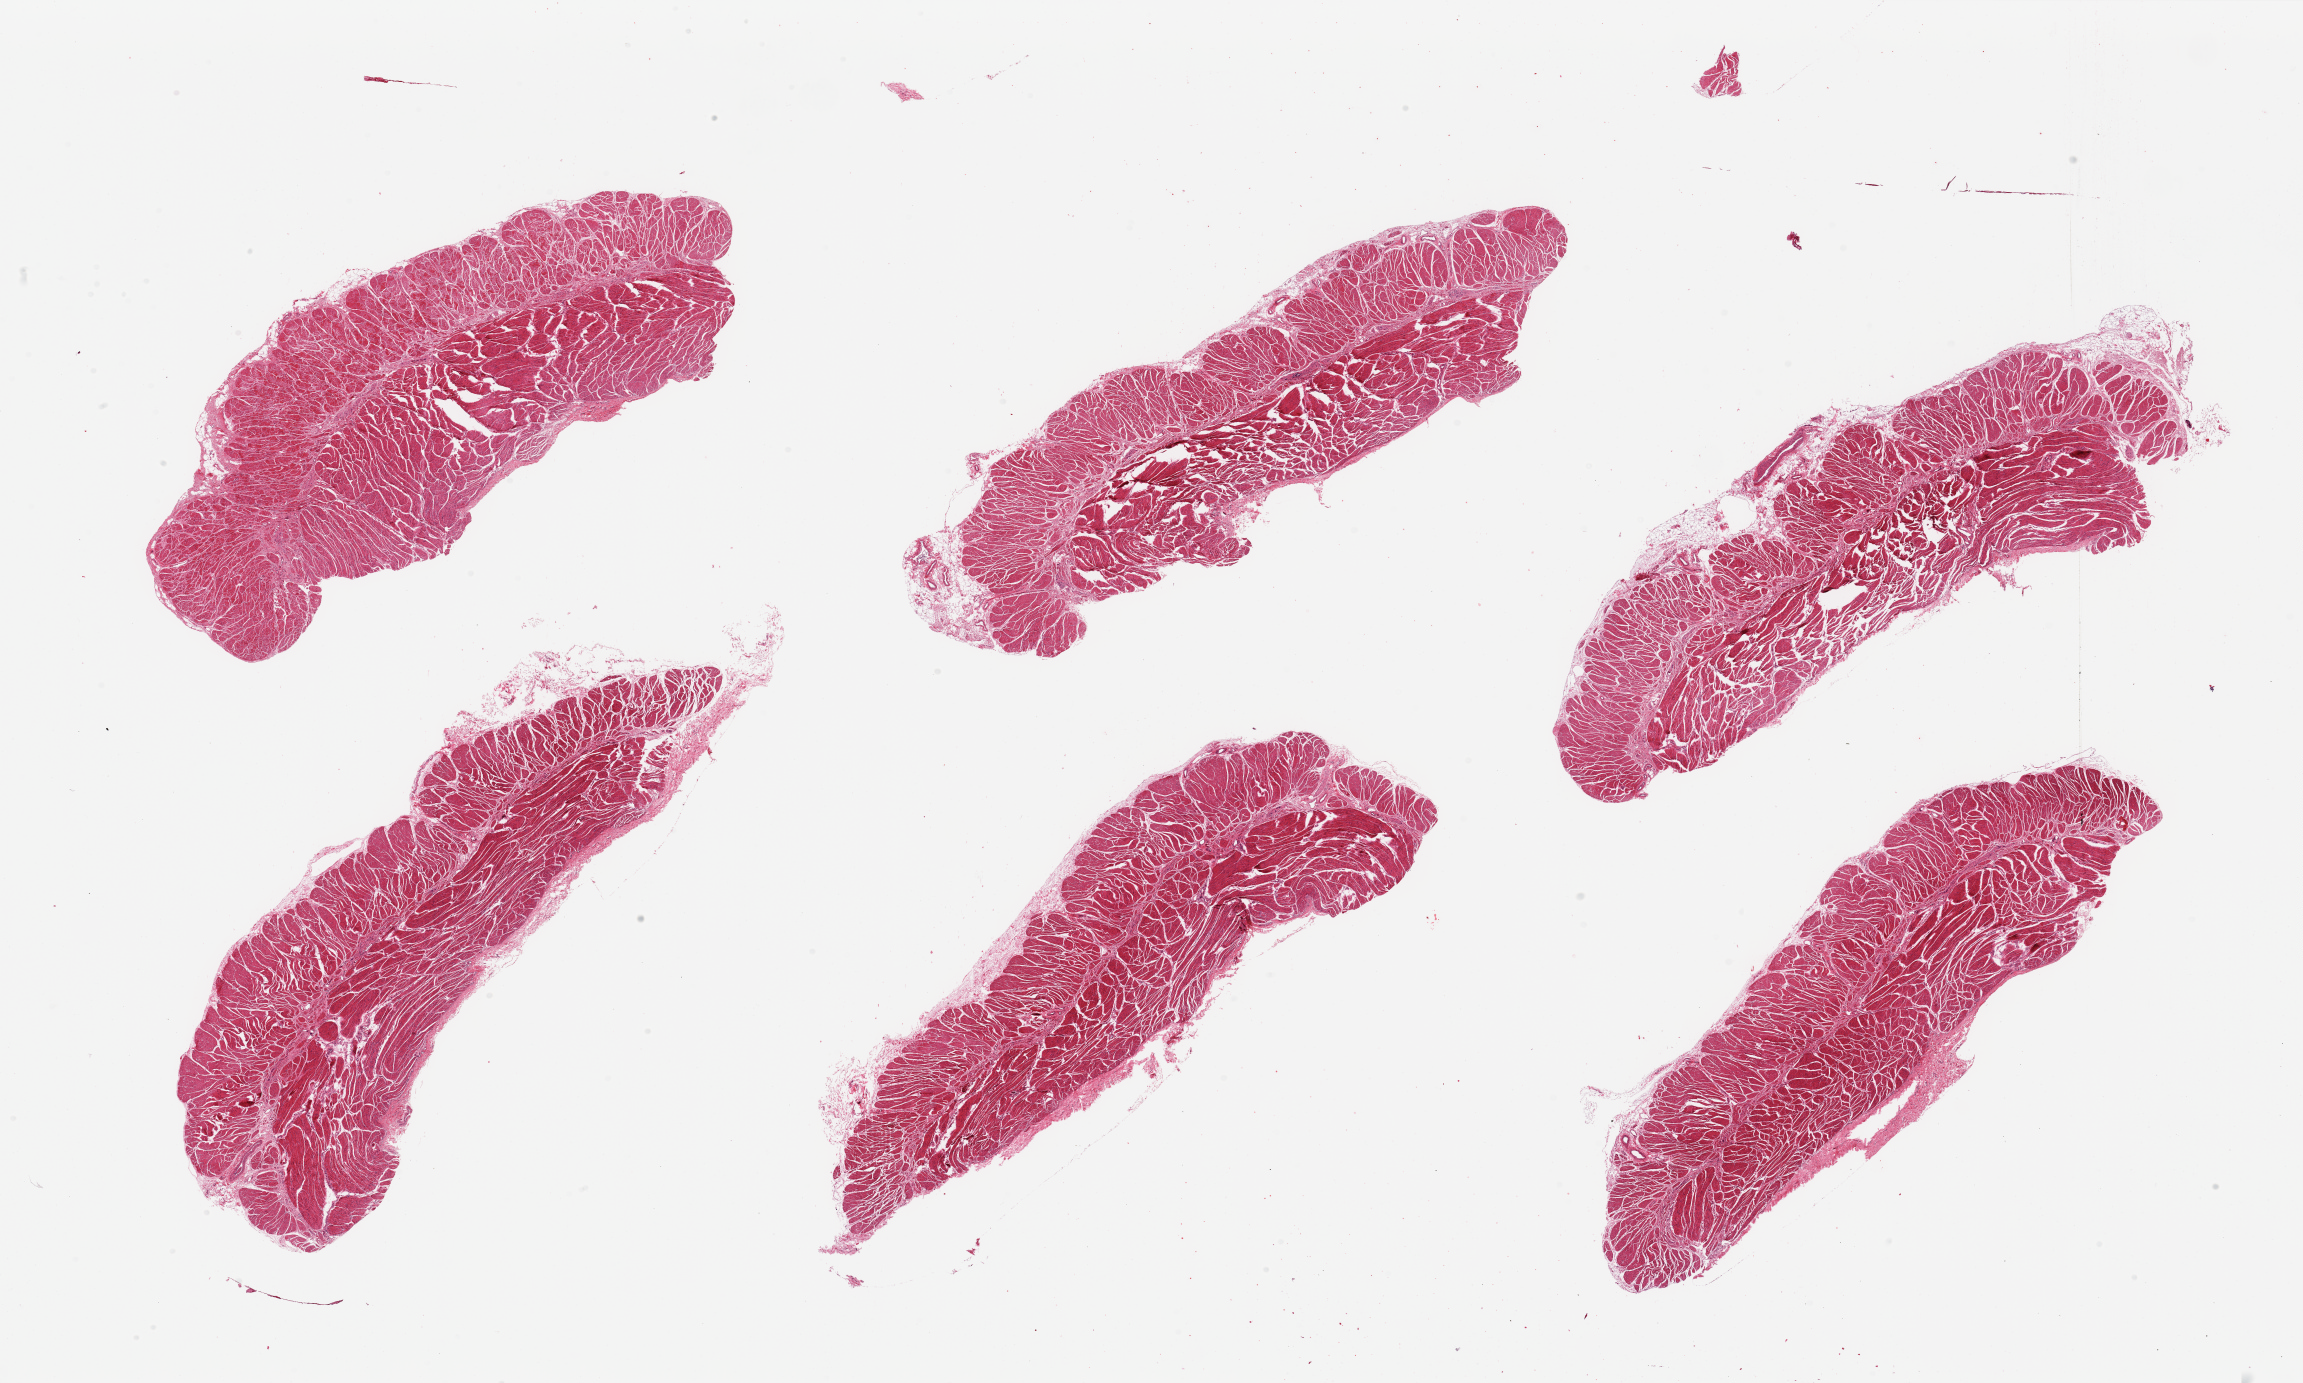
Hematoxylin and eosin (H&E) whole-slide image, a low-resolution overview of the entire scanned area, about 36.4 x 21.9 mm (from a 20x scan); PAXgene-fixed, paraffin-embedded tissue; section of gastroesophageal junction (target tissue); donor tissue sample. Male donor.
Review note (as recorded): 6 pieces, confirmed target muscularis.